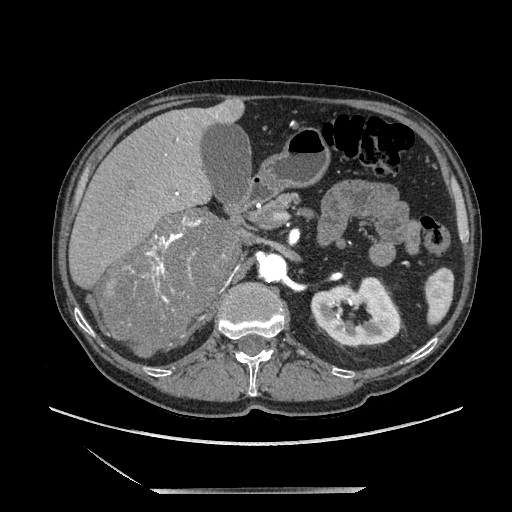
Contrast-enhanced abdominal CT, one axial slice; position 117 of 243 along the scan axis; soft-tissue window (W 400 / L 40 HU); 1.25 mm slice thickness; 512 × 512 image matrix. Male patient. Case-level facts recorded for this patient, not image findings: diagnosis: adrenocortical carcinoma; tumour side: right adrenal; tumour size at pathology: 16 cm; Ki-67 index: 17 %; stage (as recorded): 3.
Outlined on this slice (semi-automatic segmentation, software-assisted and operator-edited):
- mass: bounding box [x1, y1, x2, y2] px = [103, 210, 239, 357]